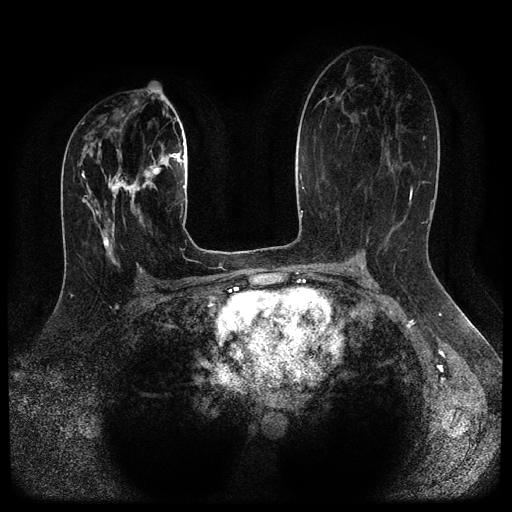
Breast MRI (dynamic contrast-enhanced, multi-phase), one axial slice. Slice 58 of 116 in the series (ordered by position). Dynamic contrast-enhanced series, time point 2 of 5 at this slice position (early post-contrast). 1.5 T. TE 2.6 ms, TR 5.4 ms. 512 × 512 image matrix, field of view 340 × 340 mm. Female patient, age 29 years.
Structures marked on this image (semi-automatic segmentation, software-assisted and operator-edited):
- breast lesion (labelled 'tumour' in the annotation; benign lesions carry a separate 'benign' label): bounding box [x1, y1, x2, y2] px = [105, 152, 162, 201]
- breast lesion (labelled benign in the annotation): [100, 228, 116, 265]